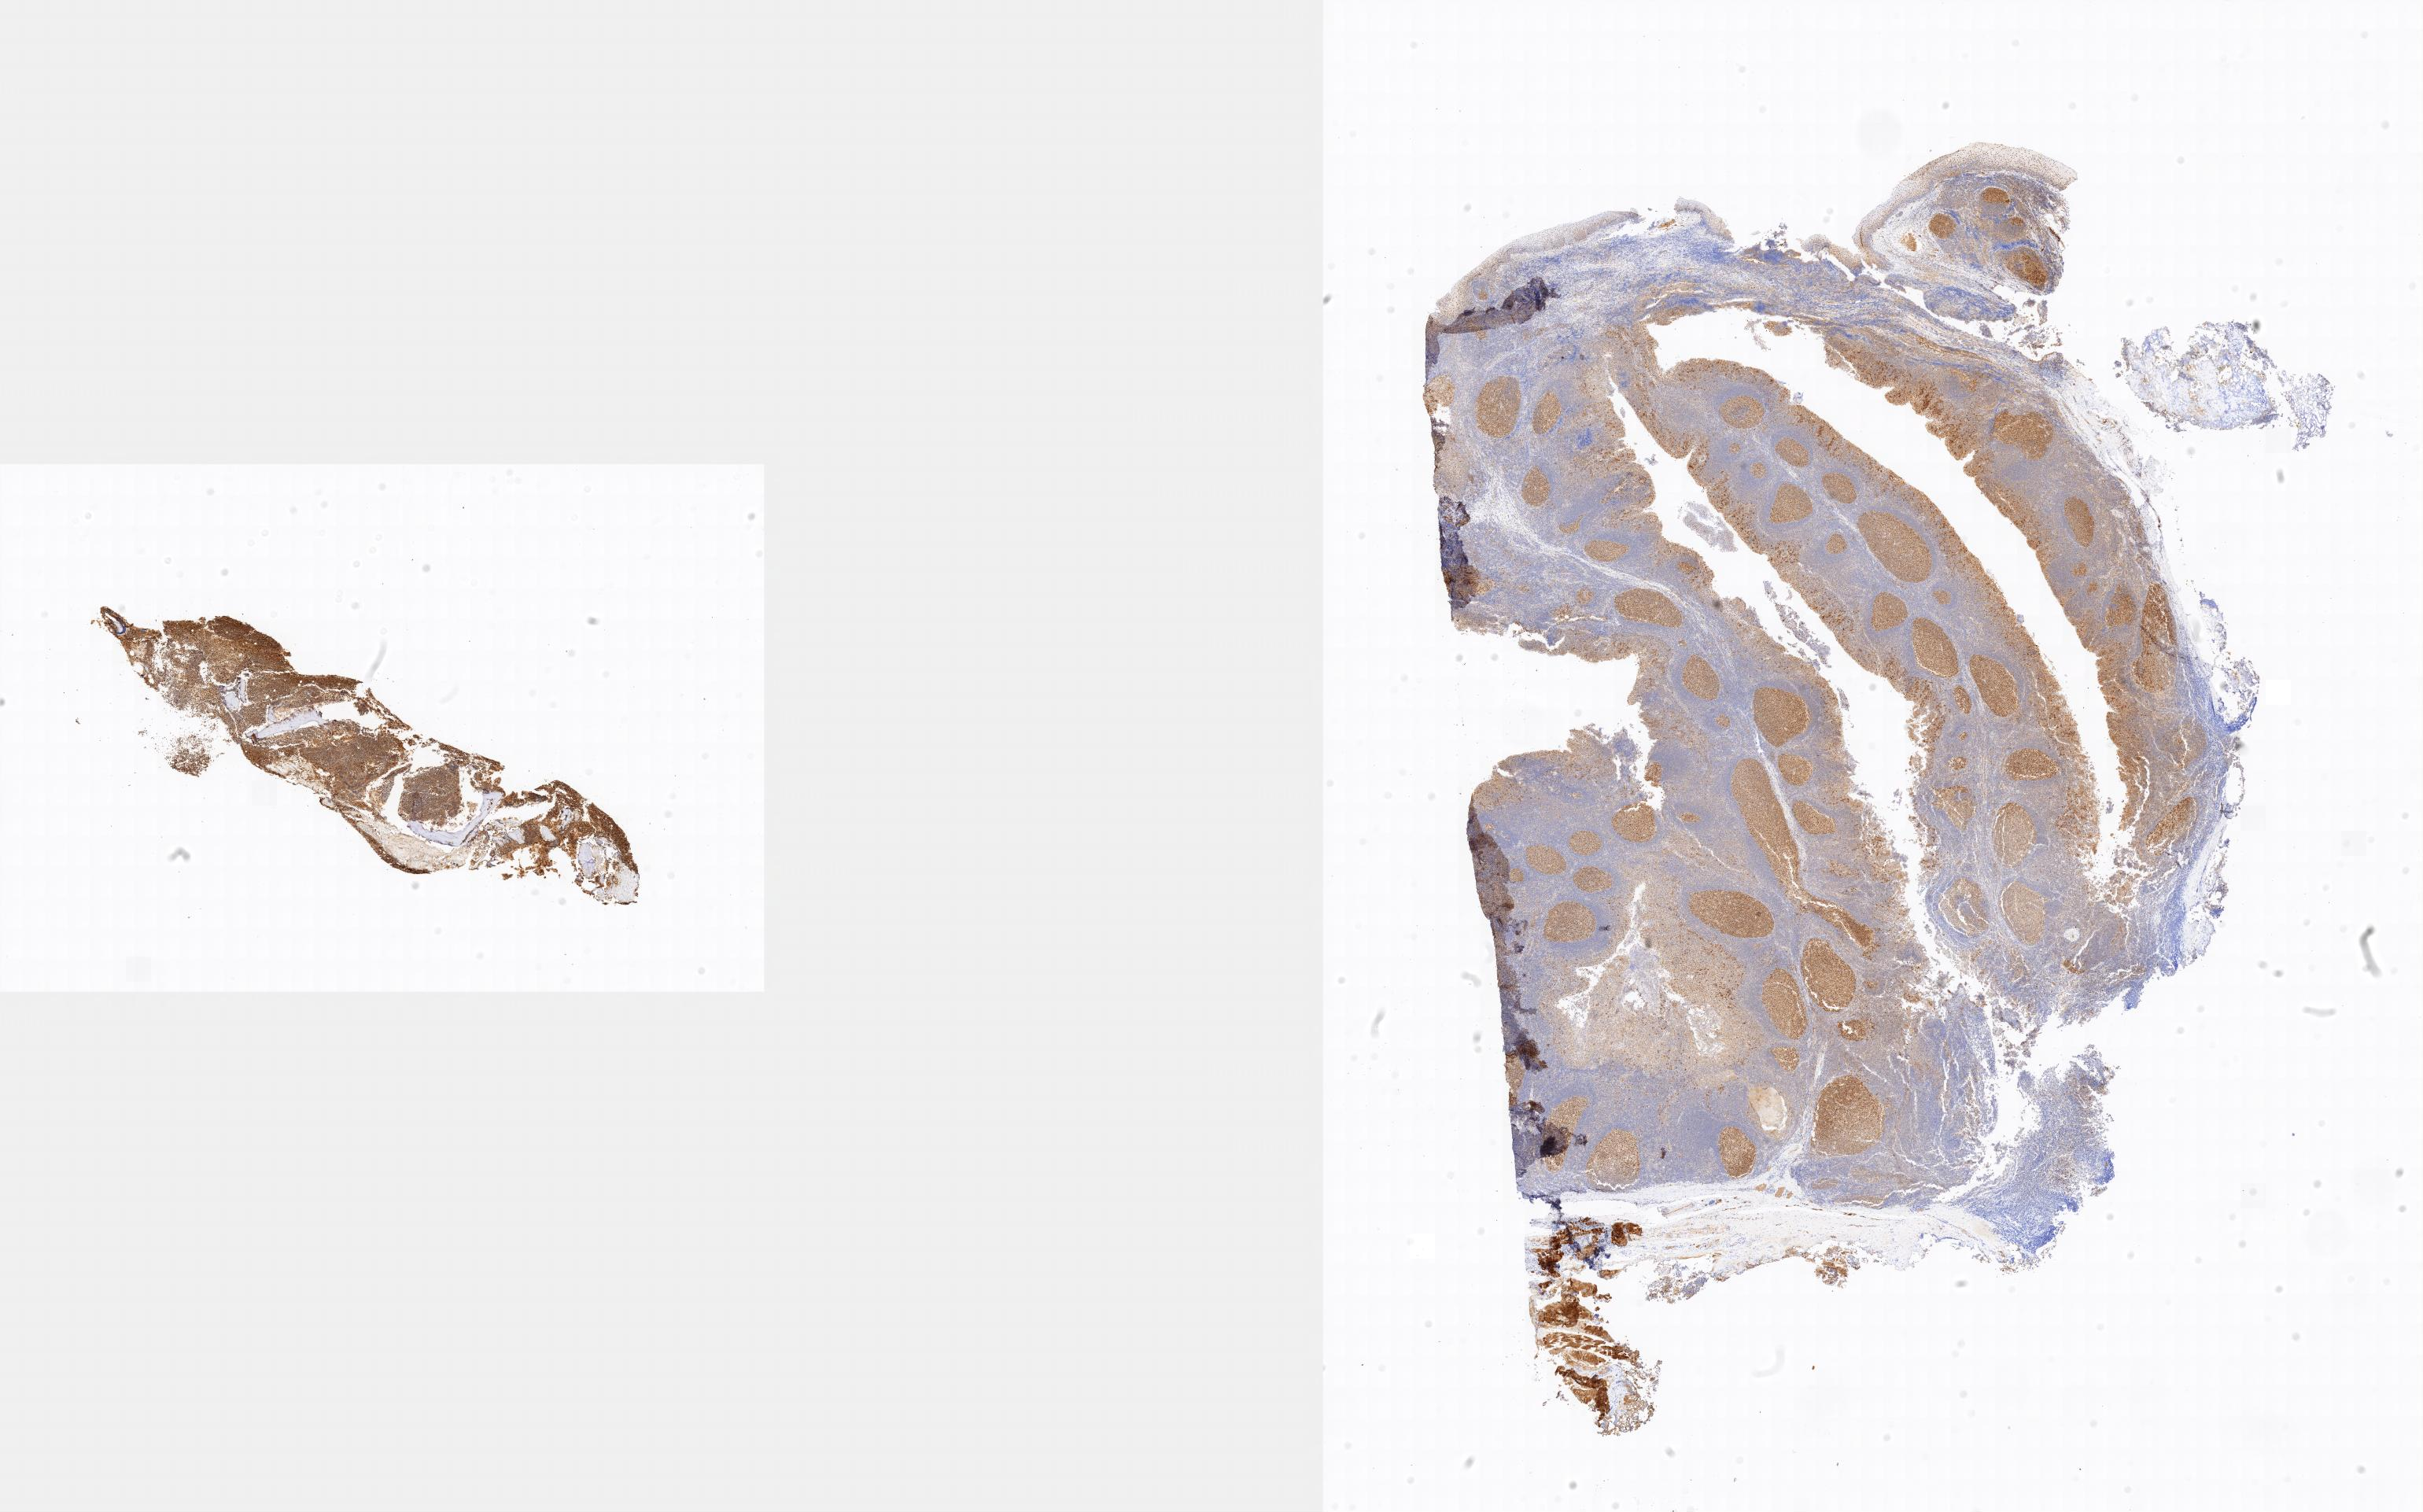
Whole-slide image, immunohistochemical stain for BCL6 — low-resolution overview of the scanned area. Specimen: tumor tissue. Site: bone marrow. Female patient; age at initial diagnosis 3 years.
Histologic diagnosis: Burkitt lymphoma, NOS.